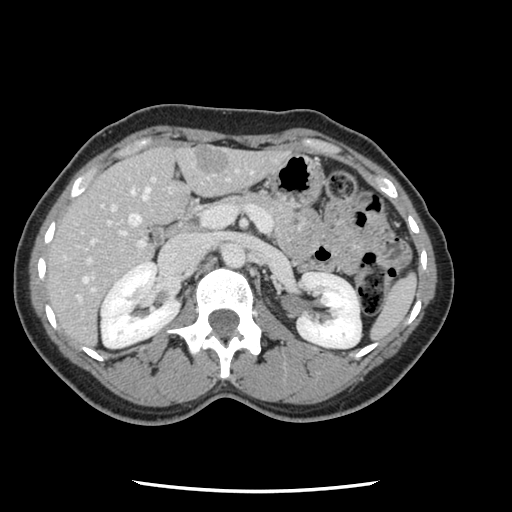
Contrast-enhanced abdominal CT, one axial slice; slice 60 of 134 in the series (ordered by position); intravenous contrast given; soft-tissue window (W 400 / L 40 HU); 512 × 512 image matrix. Female patient, age 43 years. Case-level facts recorded for this patient, not image findings: diagnosis: colorectal cancer liver metastases, imaged before liver resection; multiple liver metastases: yes; largest metastasis: 3.4 cm; disease in both lobes: yes.
Structures marked on this image (manually delineated by an expert):
- hepatic veins: box from (x=79, y=179) to (x=155, y=299) px
- liver: (x=46, y=147)–(x=287, y=348)
- planned liver remnant (the part of the liver to remain after resection): (x=46, y=148)–(x=184, y=316)
- portal vein (with intrahepatic branches): (x=85, y=171)–(x=273, y=293)
- liver metastasis: (x=195, y=151)–(x=230, y=173)